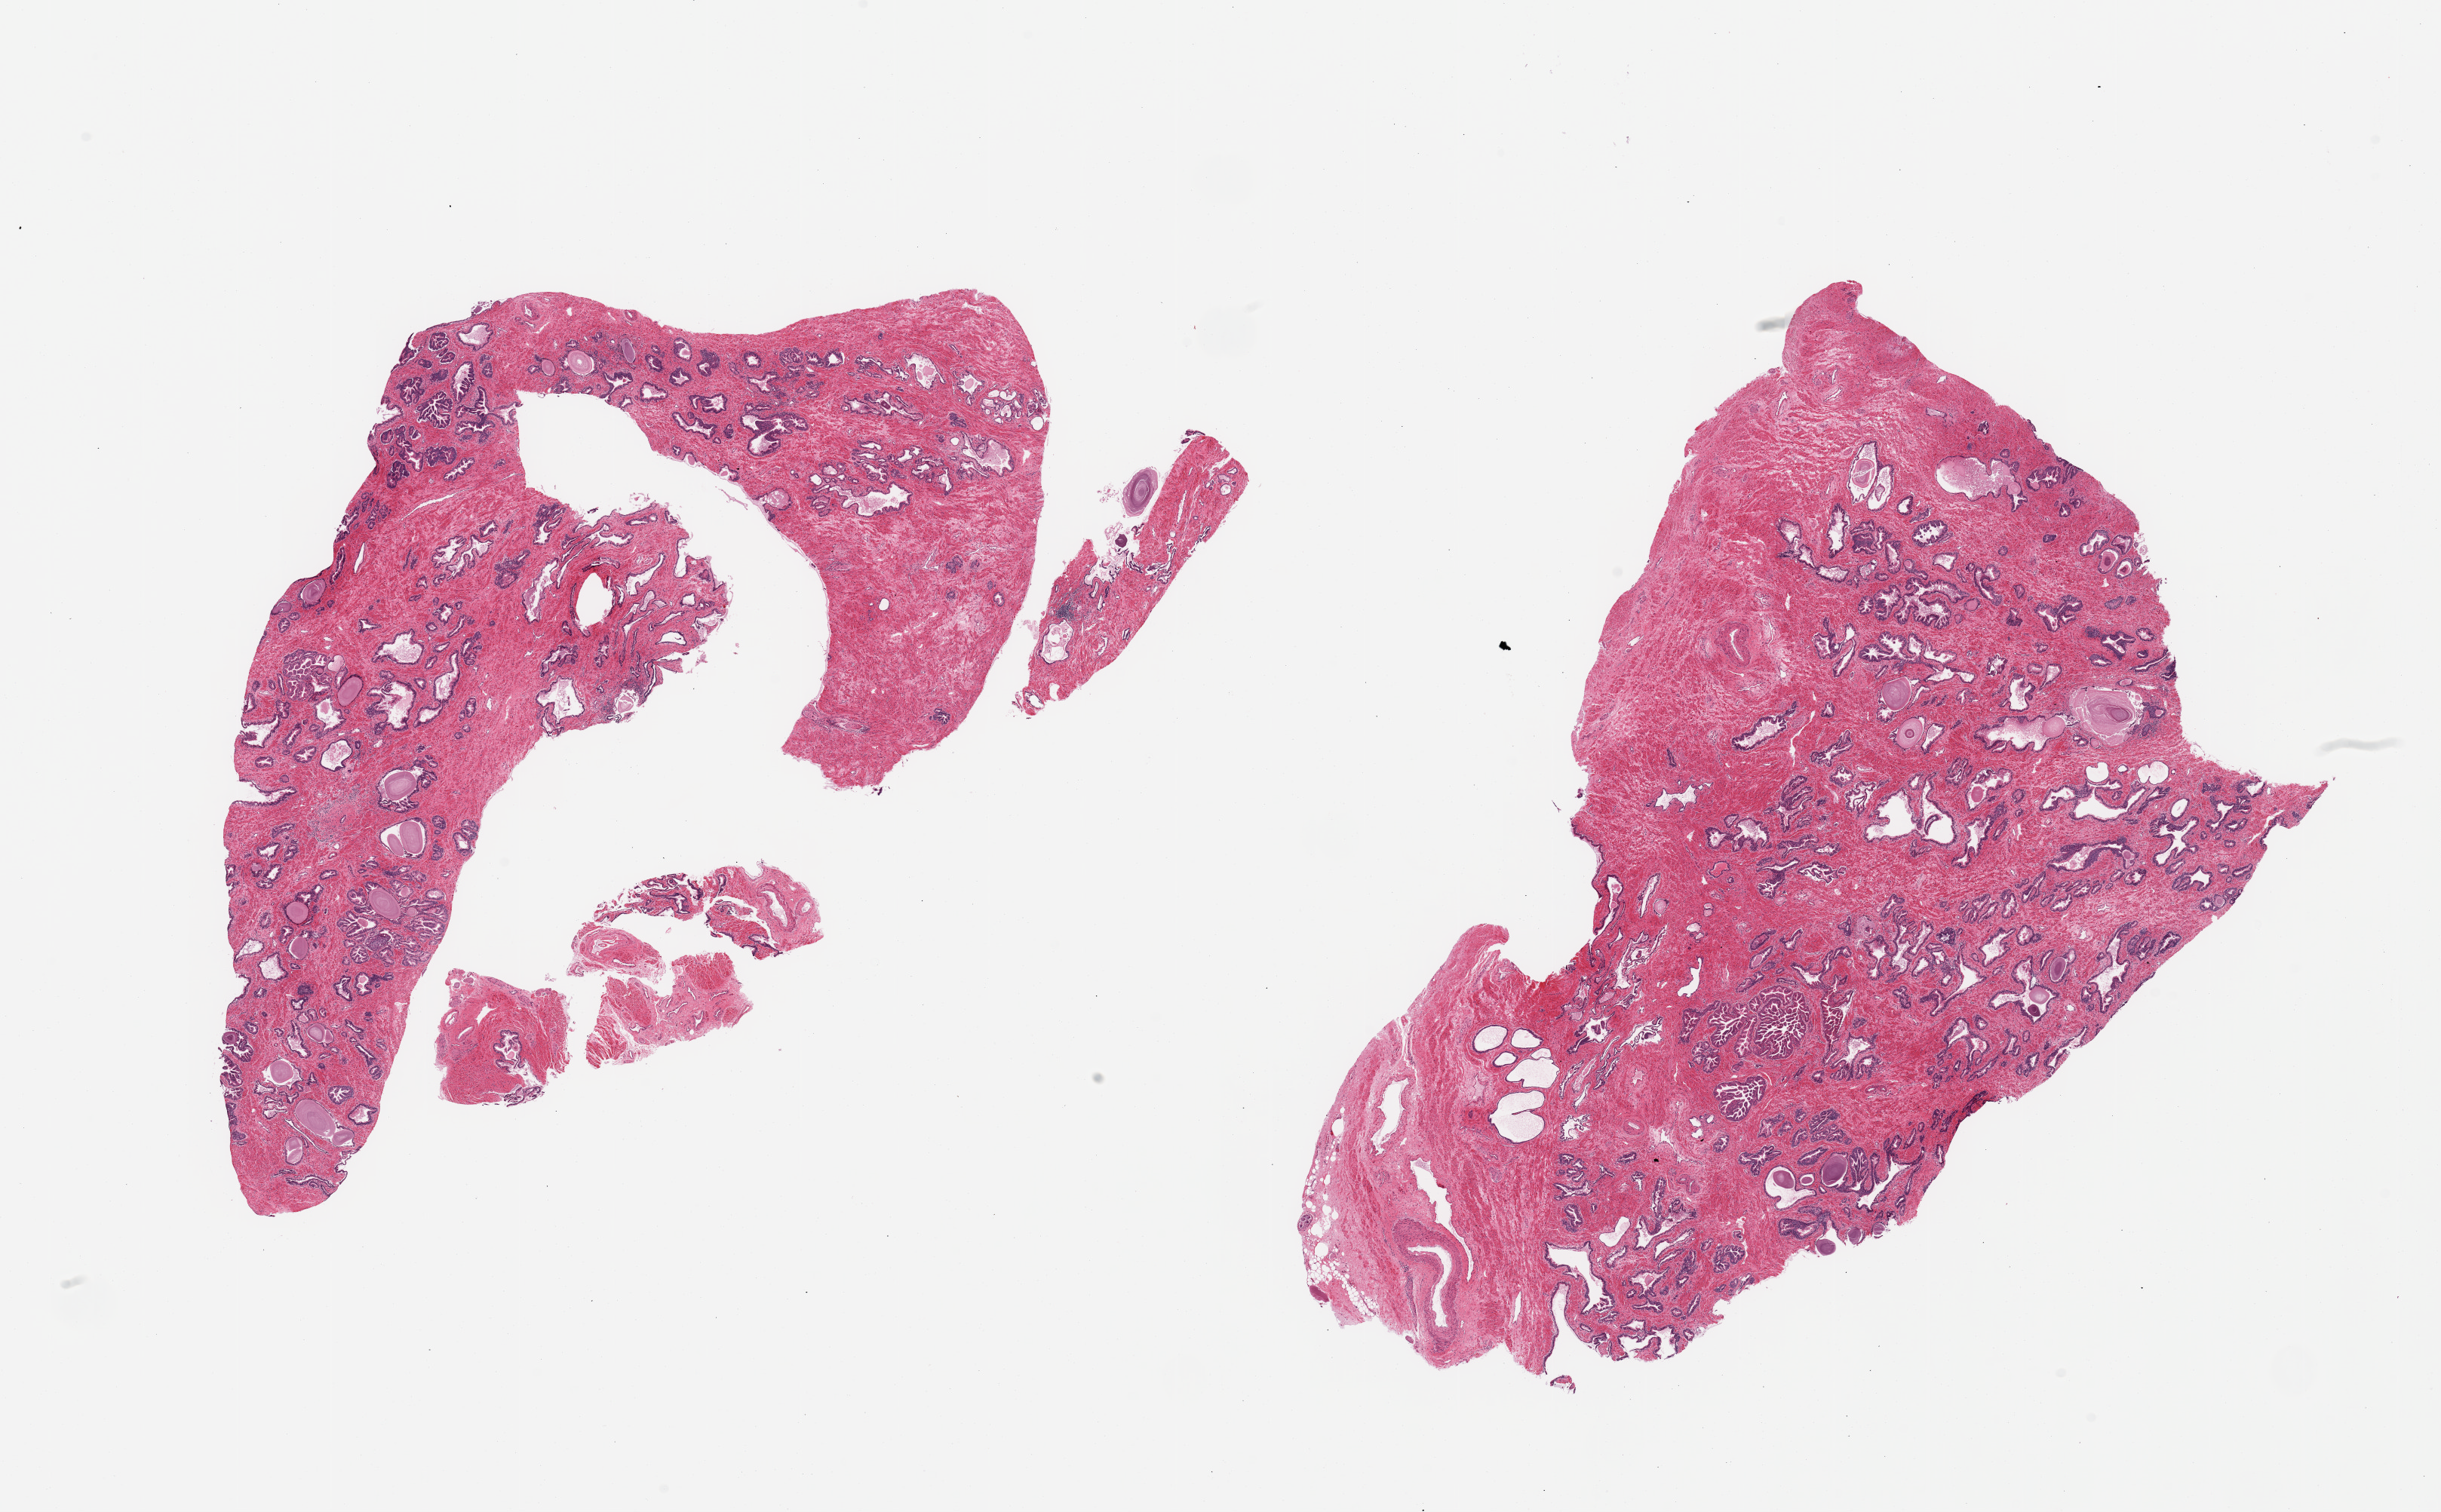
H&E whole-slide image, brightfield — shown as a low-resolution overview of the whole scanned area (about 25.6 x 15.9 mm), PAXgene-fixed, paraffin-embedded tissue, target tissue: prostate, donor tissue sample. Donor sex: male.
Reviewer comment on this tissue sample: 2 pieces, glandular hyperplastic pattern.